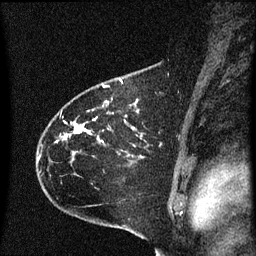
Breast MRI (dynamic contrast-enhanced), one sagittal slice; position 46 of 60 along the scan axis; dynamic contrast-enhanced series, image 2 of 3 at this slice position (ordered by acquisition); 1.5 T; TE 4.2 ms, TR 8.4 ms; 2 mm slice thickness; 256 × 256 image matrix, field of view 200 × 200 mm. Female patient, age 35 years. From the clinical record (not read from this slice): setting: breast cancer imaged before/during neoadjuvant chemotherapy; receptor status: HER2-positive.
Outlined on this slice (semi-automatic segmentation, software-assisted and operator-edited):
- analysis volume of interest (the breast-tissue region the enhancement analysis was run in; not a lesion): box from (x=39, y=68) to (x=173, y=173) px
- tumour enhancement mask (voxels above the 70 % enhancement threshold inside the analysis volume of interest): (x=64, y=124)–(x=83, y=137)